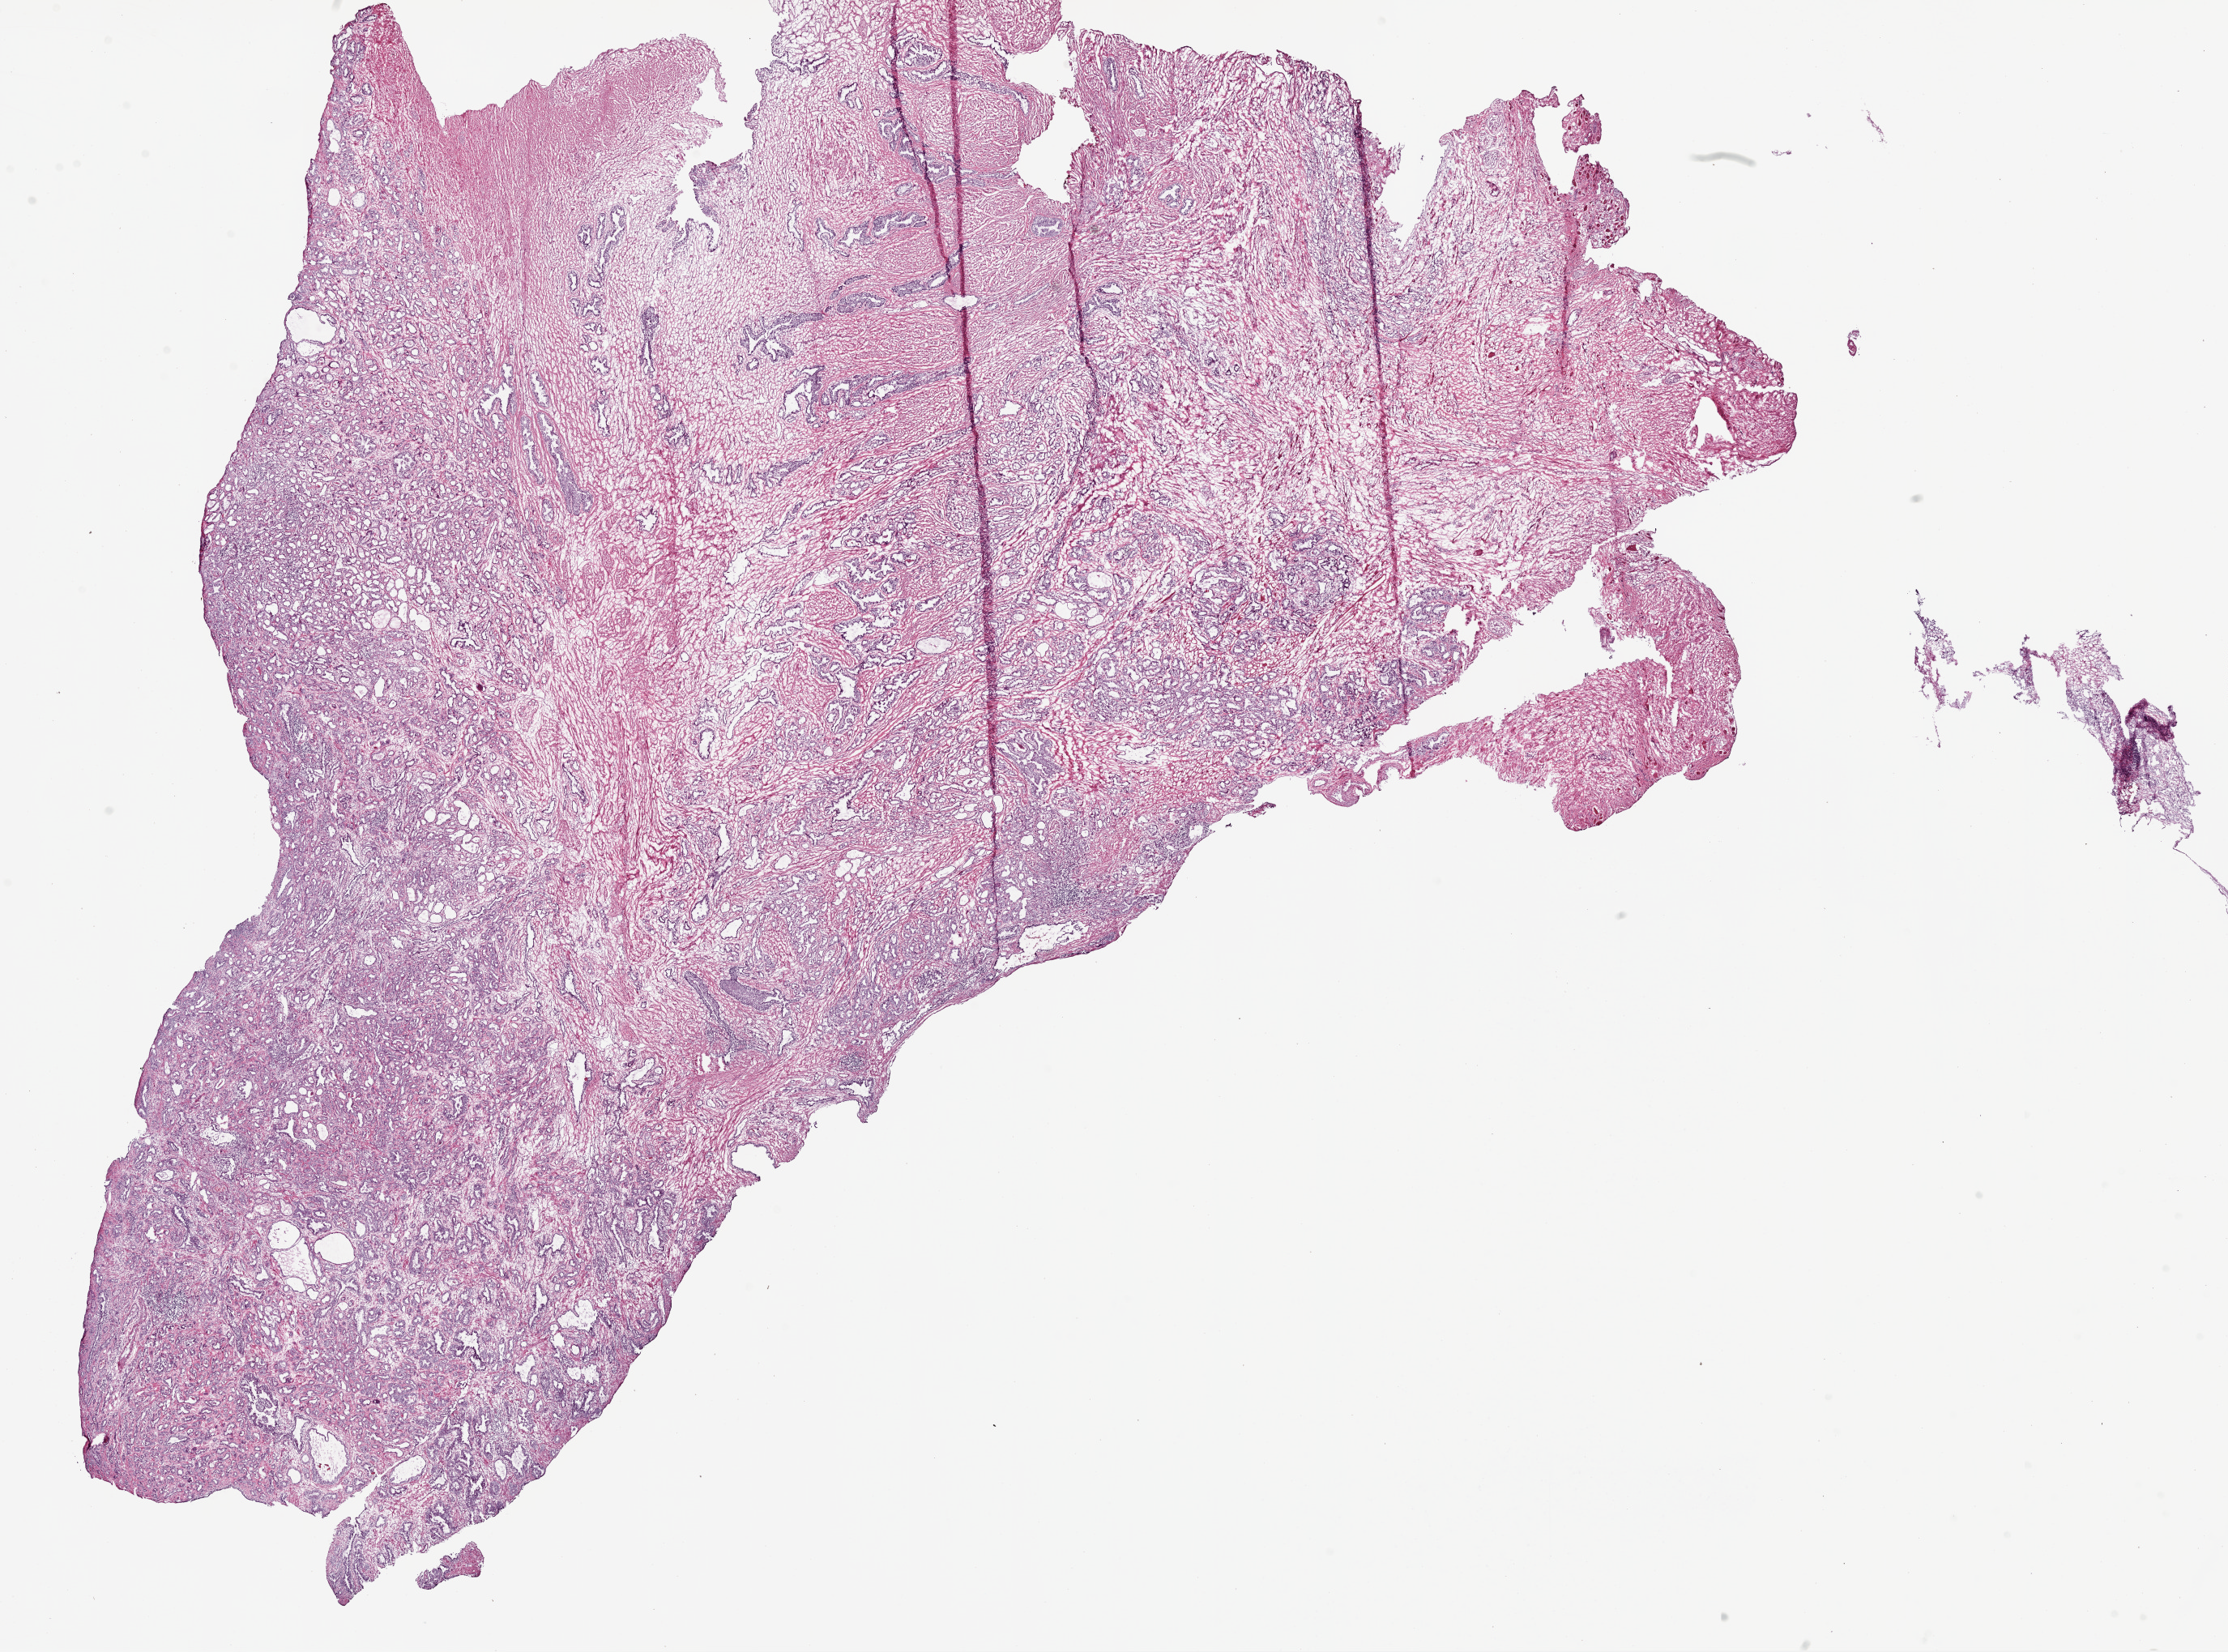
Hematoxylin and eosin (H&E) stained whole-slide image, whole scanned area (about 22.1 x 16.4 mm) shown as a low-resolution overview; frozen section; prostate, primary tumour sample. Male patient; age at initial diagnosis 50 years. Composition of this section per pathologist review: tumour cells 40%, tumour nuclei 45%.
Pathologic diagnosis: Acinar cell carcinoma (prostate gland).